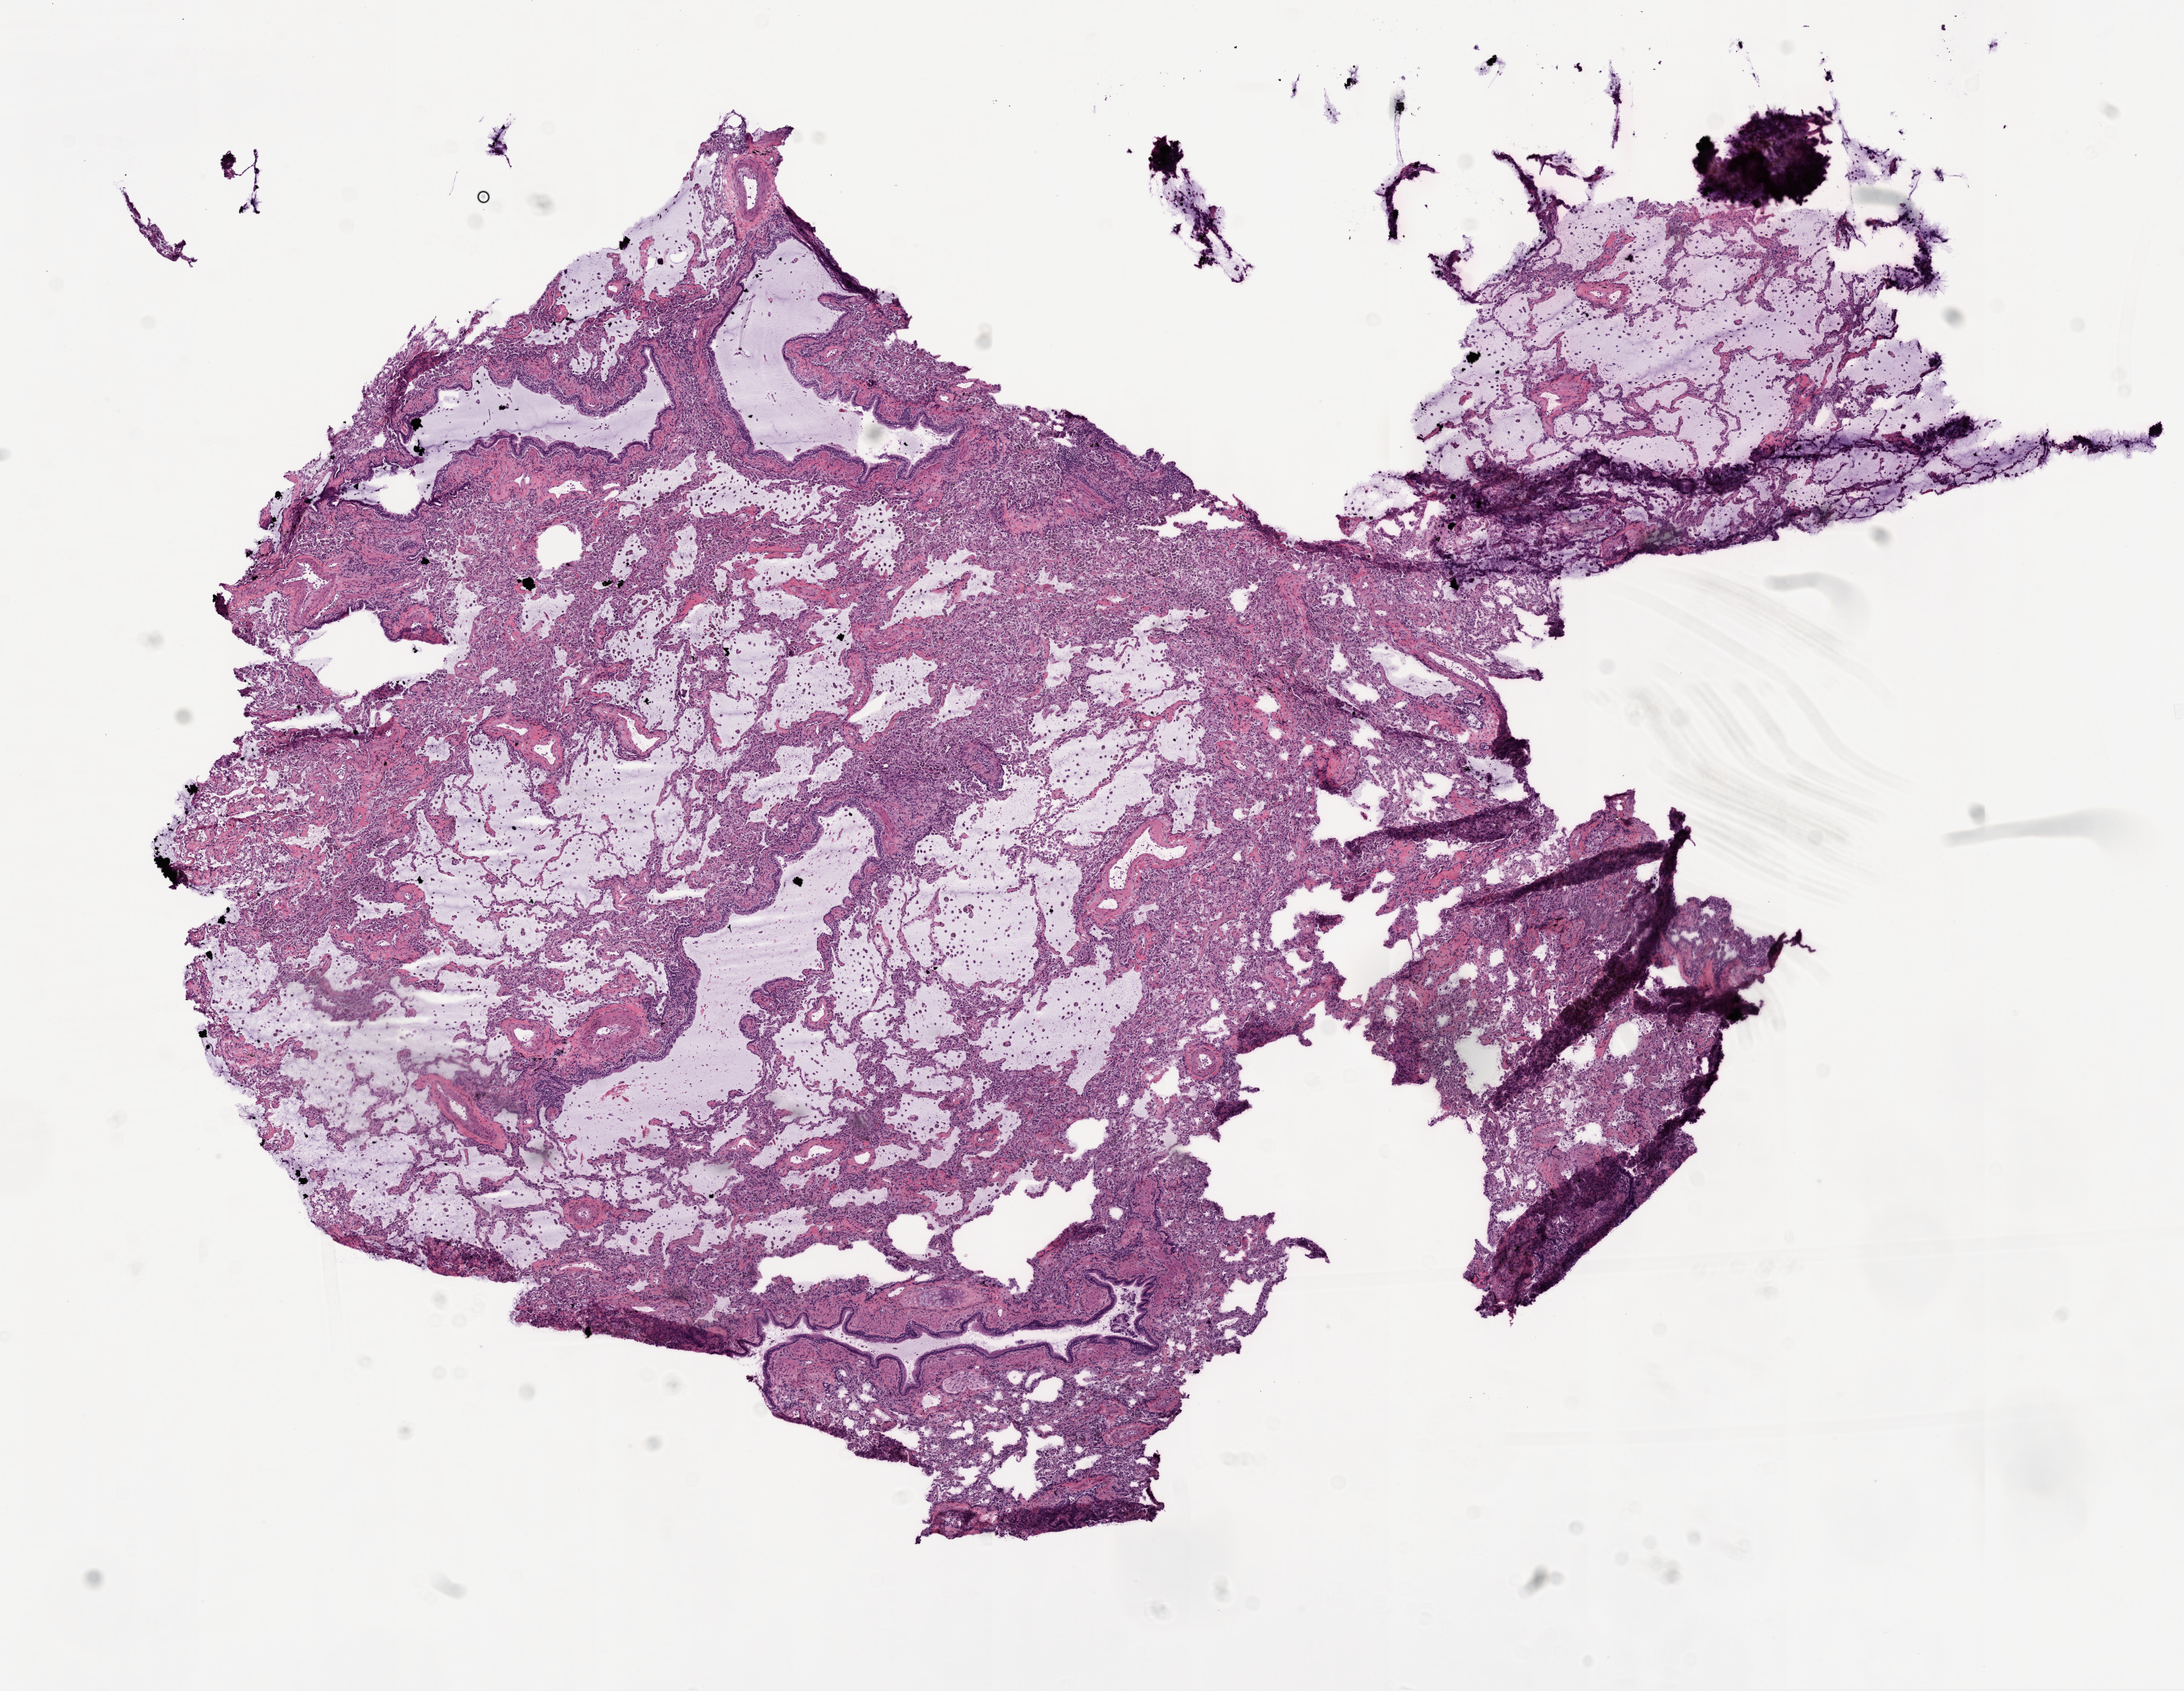
Digitized H&E-stained tissue section (whole slide) — low-resolution overview of the scanned area, about 11.0 x 8.5 mm (from a 20x scan), frozen section, solid tissue normal (non-tumour tissue) sample from the lung. Patient: female, age at initial diagnosis 64 years.
* this section: solid tissue normal (non-tumour) sample from the same patient
* patient diagnosis: Squamous cell carcinoma, NOS (lower lobe, lung)